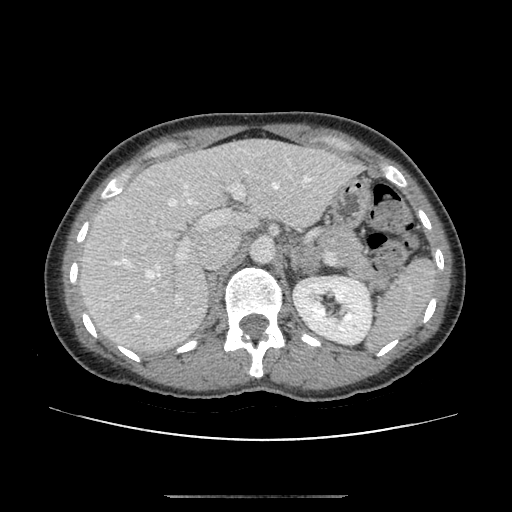
Contrast-enhanced abdominal CT, one axial slice; slice 69 of 179 in the series (ordered by position); 120 kVp; soft-tissue window (W 400 / L 40 HU); 2.5 mm slice thickness; 512 × 512 image matrix. Patient: female, 51 years. From the clinical record (not read from this slice): diagnosis: adrenocortical carcinoma; tumour side: left adrenal; tumour size at pathology: 3.5 cm; Ki-67 index: 45 %; stage (as recorded): 1.
Outlined on this slice (semi-automatic segmentation, software-assisted and operator-edited):
- mass: bounding box (x1, y1, x2, y2) in pixels: (296, 248, 320, 274)